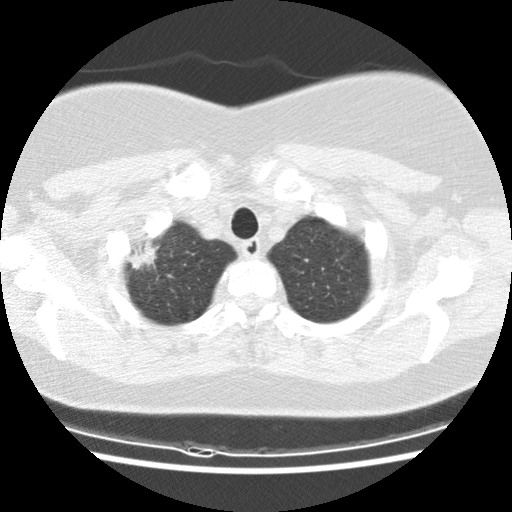
Axial slice from a low-dose chest CT screening exam. Baseline annual screen. Lung window (W 1500 / L -600 HU). 2.5 mm slice thickness. Slice 13 of 132 in the series. 512 × 512 image matrix. Female participant, aged 61 years at enrolment. Former smoker at enrolment.
Lesion marked by an expert reader, bounding box (x1, y1, x2, y2) in pixels: (114, 229, 171, 284). The exam's reader record, not a measurement of the box and not confirmed to be the same lesion: non-calcified nodule or mass ≥4 mm, right upper lobe, 26 × 16 mm, spiculated (stellate) margins, mixed attenuation. Later outcome: lung cancer diagnosed 47 days after this screen — bronchiolo-alveolar carcinoma, mixed mucinous and non-mucinous, right upper lobe, well differentiated (G1), stage IA (AJCC 6th edition), 25 mm at pathology.